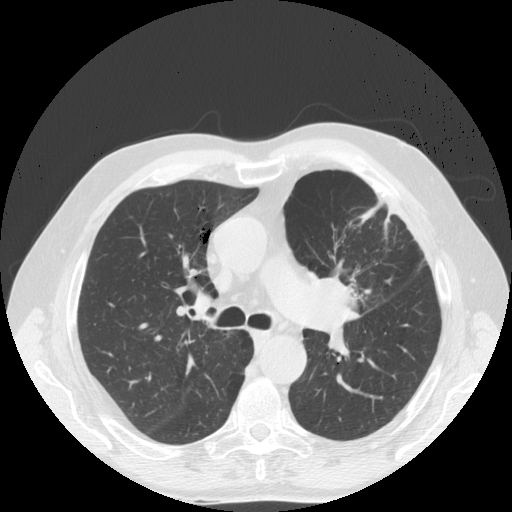
Axial slice from a low-dose chest CT screening exam. Baseline screening round. Lung window (W 1500 / L -600 HU). Slice 58 of 171 in the series. 512 × 512 image matrix. Male, age 70 years at enrolment.
Expert-annotated lung lesion, bounding box [x1, y1, x2, y2] px = [290, 254, 379, 344]. The exam's reader record, not a measurement of the box and not confirmed to be the same lesion: non-calcified nodule or mass ≥4 mm, left upper lobe, 46 × 31 mm, spiculated (stellate) margins, soft tissue attenuation.